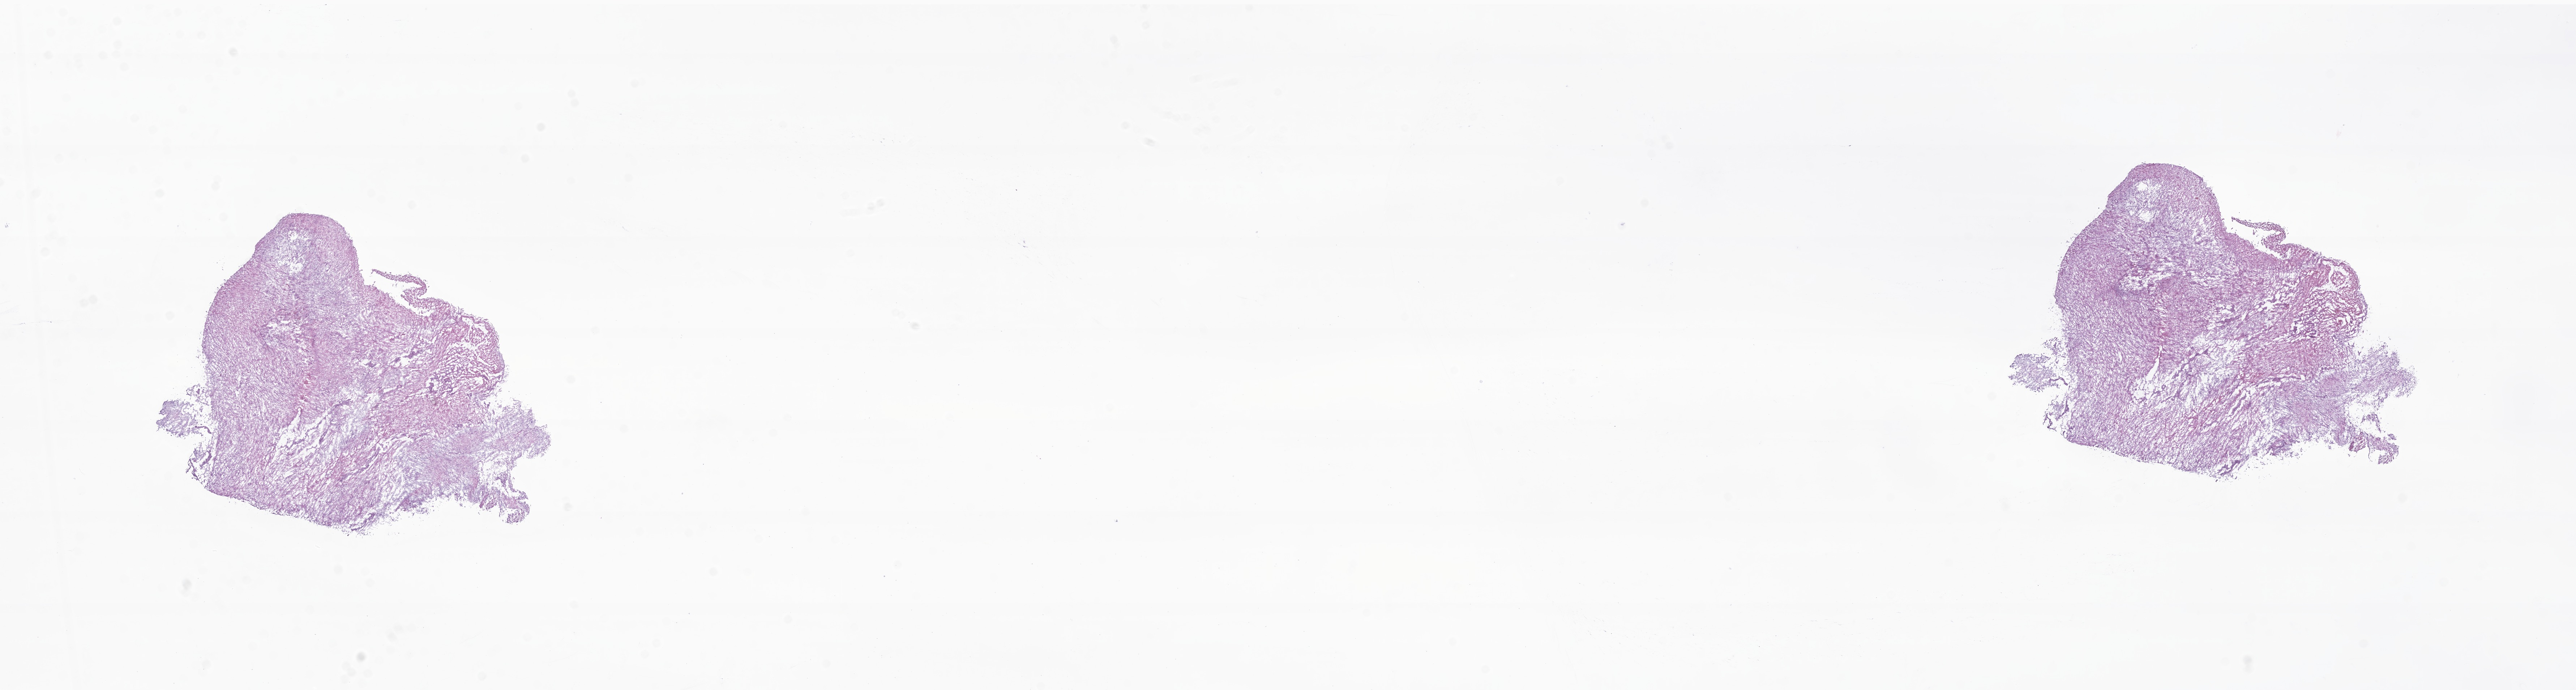
Digitized haematoxylin and eosin-stained section of tumor tissue from the brain — low-resolution overview of the scanned area, about 30.0 x 8.0 mm; cryosection (OCT / tissue freezing medium). Patient: female, age 63 months (5 years 3 months).
Recorded diagnosis: Pilocytic astrocytoma.